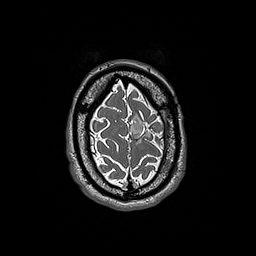
Brain MRI from a brain-tumour surgery series, one axial slice. Slice 40 of 192 in the series (ordered by position). 1 mm slice thickness. 256 × 256 image matrix. Case-level facts recorded for this patient, not image findings: histopathology: Oligodendroglioma; WHO grade: 3; IDH mutation: yes; tumour location: Left Frontal.
Structures marked on this image (manually delineated by an expert):
- tumour: bounding box [x1, y1, x2, y2] px = [130, 116, 146, 143]